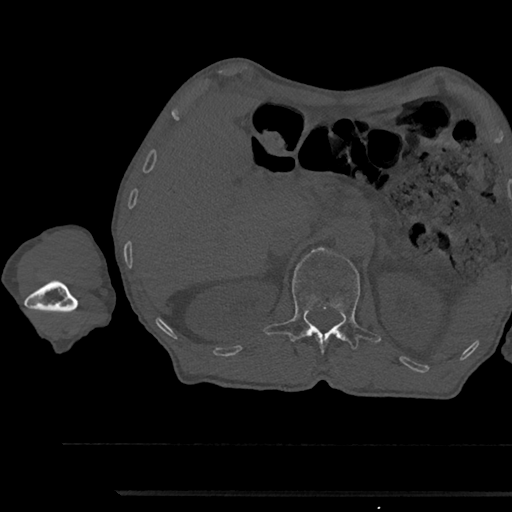
CT including the spine, one axial slice. Slice 647 of 797 in the series (ordered by position). Reconstruction kernel Br40s/3. Bone window (W 1800 / L 400 HU). 512 × 512 image matrix, field of view 367 × 367 mm. Patient: male, 79 years. Case-level facts recorded for this patient, not image findings: primary cancer: prostate.
Structures marked on this image (semi-automatic segmentation, software-assisted and operator-edited):
- L1 vertebra: bounding box <263,247,380,354> (left, top, right, bottom; pixels)